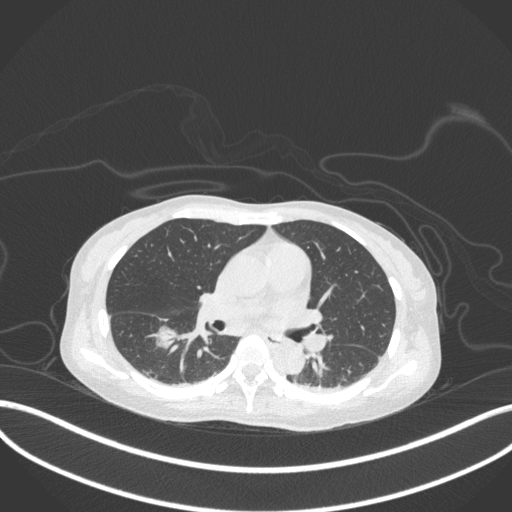
Chest CT, one axial slice. Slice 168 of 260 in the series (ordered by position). Reconstruction kernel B31f. 120 kVp. Lung window (W 1500 / L -600 HU). 1 mm slice thickness. 512 × 512 image matrix, field of view 400 × 400 mm. Patient: female, 44 years. From the clinical record (not read from this slice): clinical TNM (as recorded): T1c N0 M0.
Annotated regions visible in this slice (rectangle marked by the reading radiologist):
- lung tumour (recorded histology: adenocarcinoma): box from (x=151, y=323) to (x=183, y=356) px